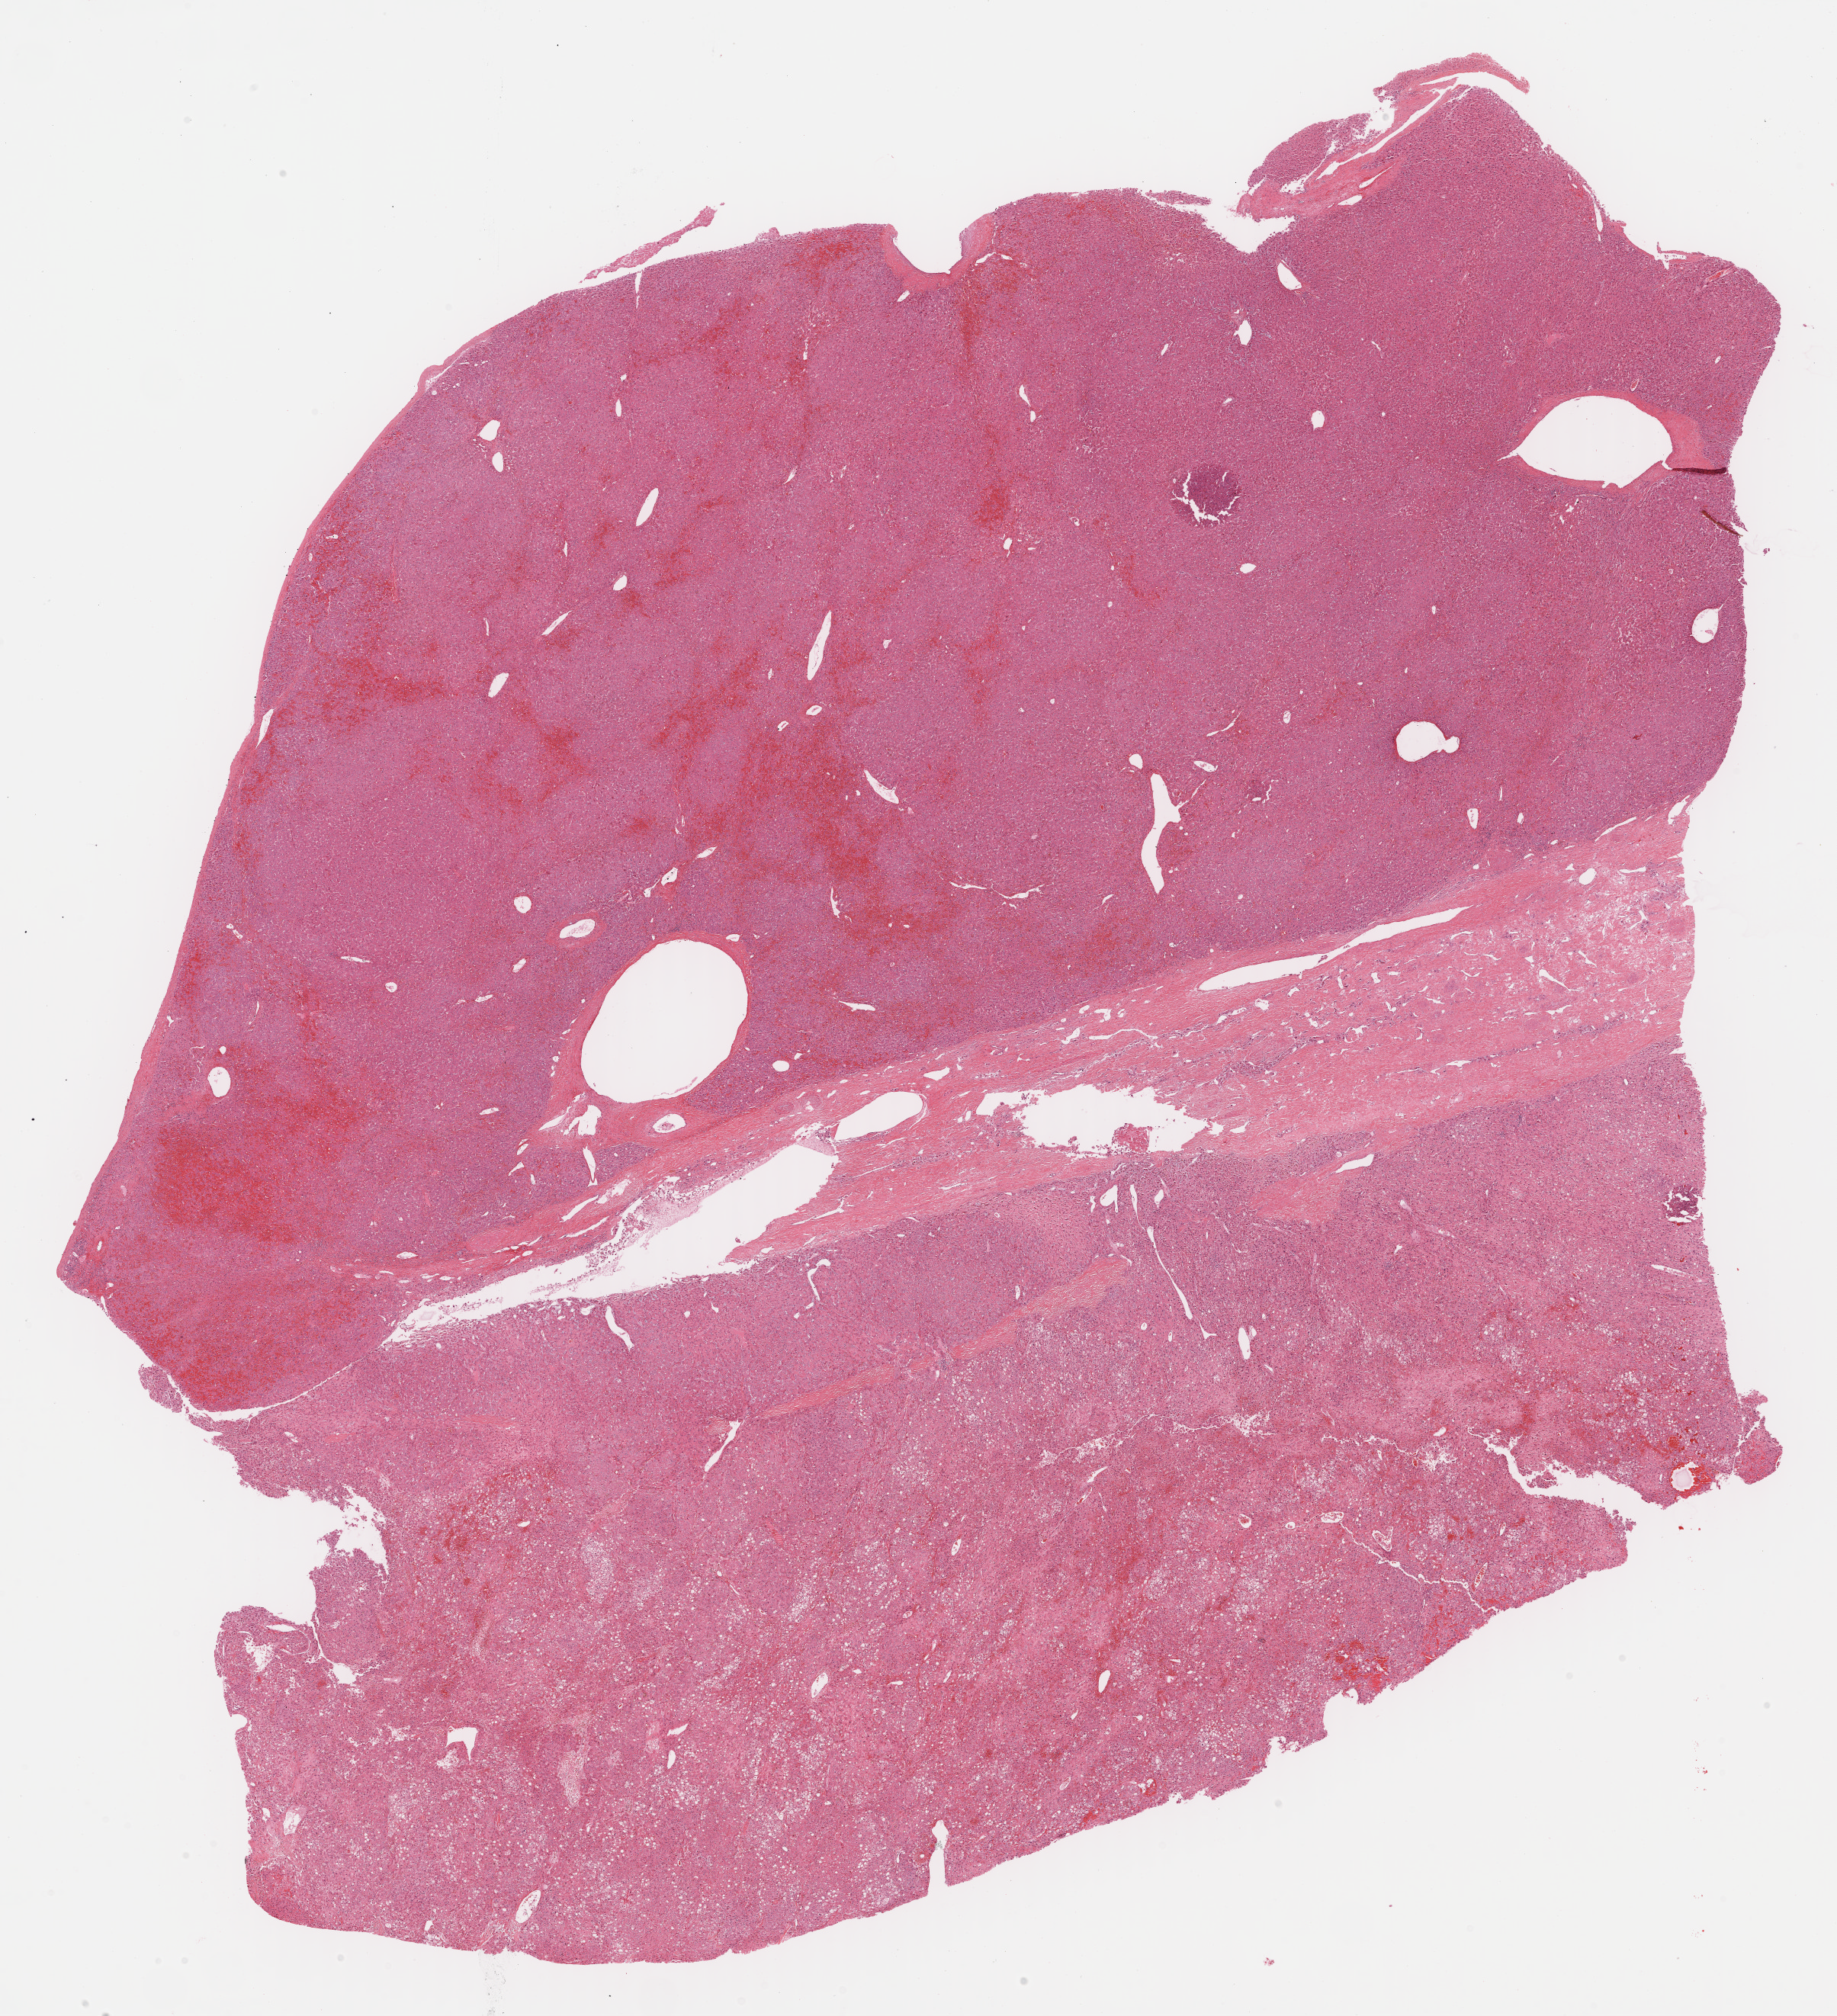
Whole-slide histology image, Hematoxylin and eosin (H&E) stained, low-resolution overview of the scanned area, about 19.5 x 21.4 mm (acquisition: 40x scan). FFPE section. Primary tumour sample from the liver. Male, age 37 years at initial diagnosis. Histologic grade: G3 (poorly differentiated).
AJCC pathologic stage: IIIA (5th edition). TNM: T3 N0 M0. Diagnosis: Hepatocellular carcinoma, NOS.